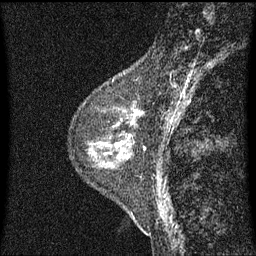
Breast MRI (dynamic contrast-enhanced), one sagittal slice; slice 18 of 60 in the series (ordered by position); dynamic contrast-enhanced series, image 2 of 3 at this slice position (ordered by acquisition); 1.5 T; TE 4.2 ms, TR 8 ms; 256 × 256 image matrix, field of view 200 × 200 mm. Patient: female, 48 years.
Annotated regions visible in this slice (semi-automatically segmented with operator editing):
- analysis volume of interest (the breast-tissue region the enhancement analysis was run in; not a lesion): box from (x=103, y=74) to (x=145, y=139) px
- tumour enhancement mask (voxels above the 70 % enhancement threshold inside the analysis volume of interest): (x=112, y=102)–(x=142, y=139)